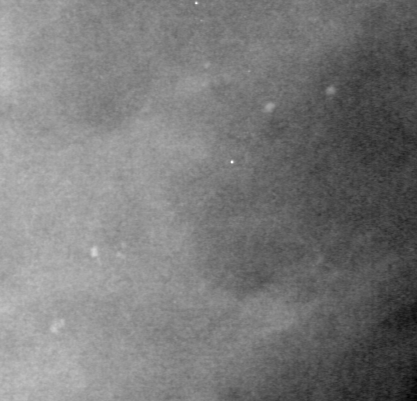
Crop from a digitized film mammogram around one marked abnormality; right breast; MLO view.
Calcifications, morphology pleomorphic, distribution segmental; BI-RADS assessment category 4; subtlety rating 3 on a 1 (subtle) to 5 (obvious) scale; pathology result (as recorded, not read from the image): benign.